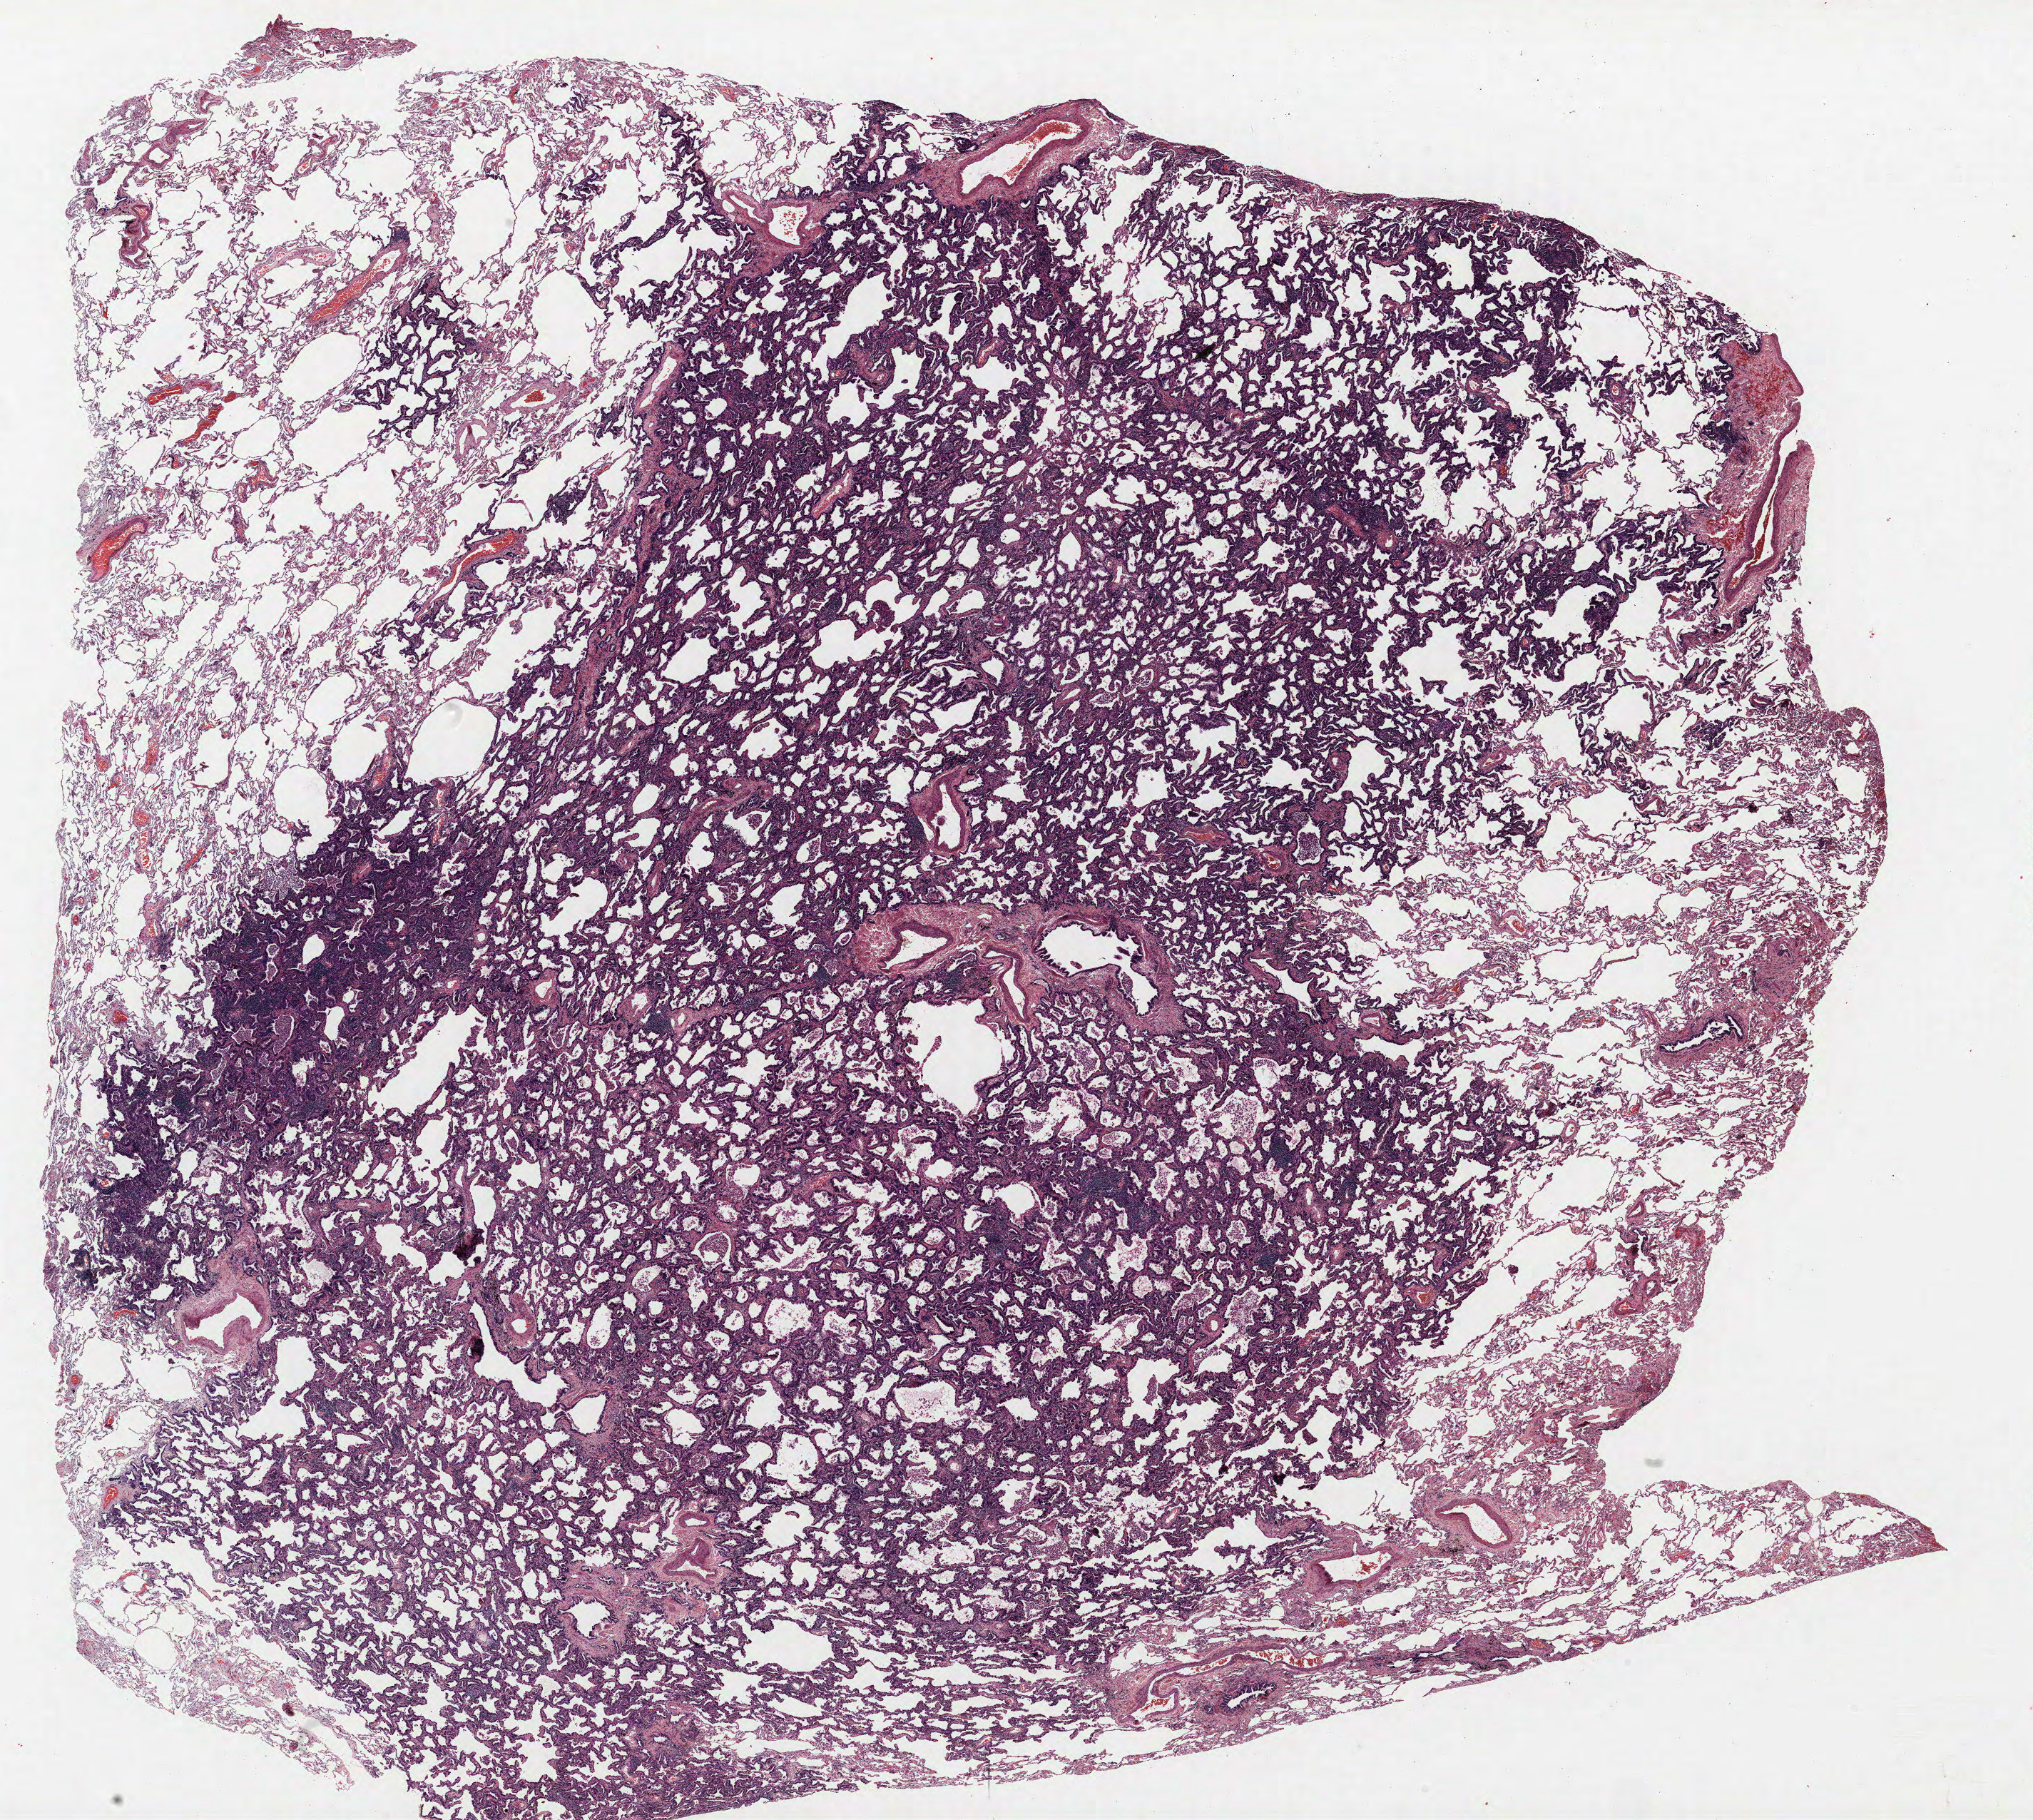
H&E-stained whole-slide image — low-resolution overview of the scanned area, about 22.8 x 20.4 mm (slide scanned at 40x). Formalin-fixed paraffin-embedded (FFPE) section. Lung tissue. Female patient, aged 56 at enrolment. Former smoker at enrolment. Grade: well differentiated (G1).
* tumour size (pathology): 25 mm
* primary tumour location (clinical record): left upper lobe
* ICD-O-3 topography: upper lobe of lung (C34.1)
* stage (AJCC 6th edition): IA
* participant's lung-cancer diagnosis: Bronchiolo-alveolar carcinoma, non-mucinous